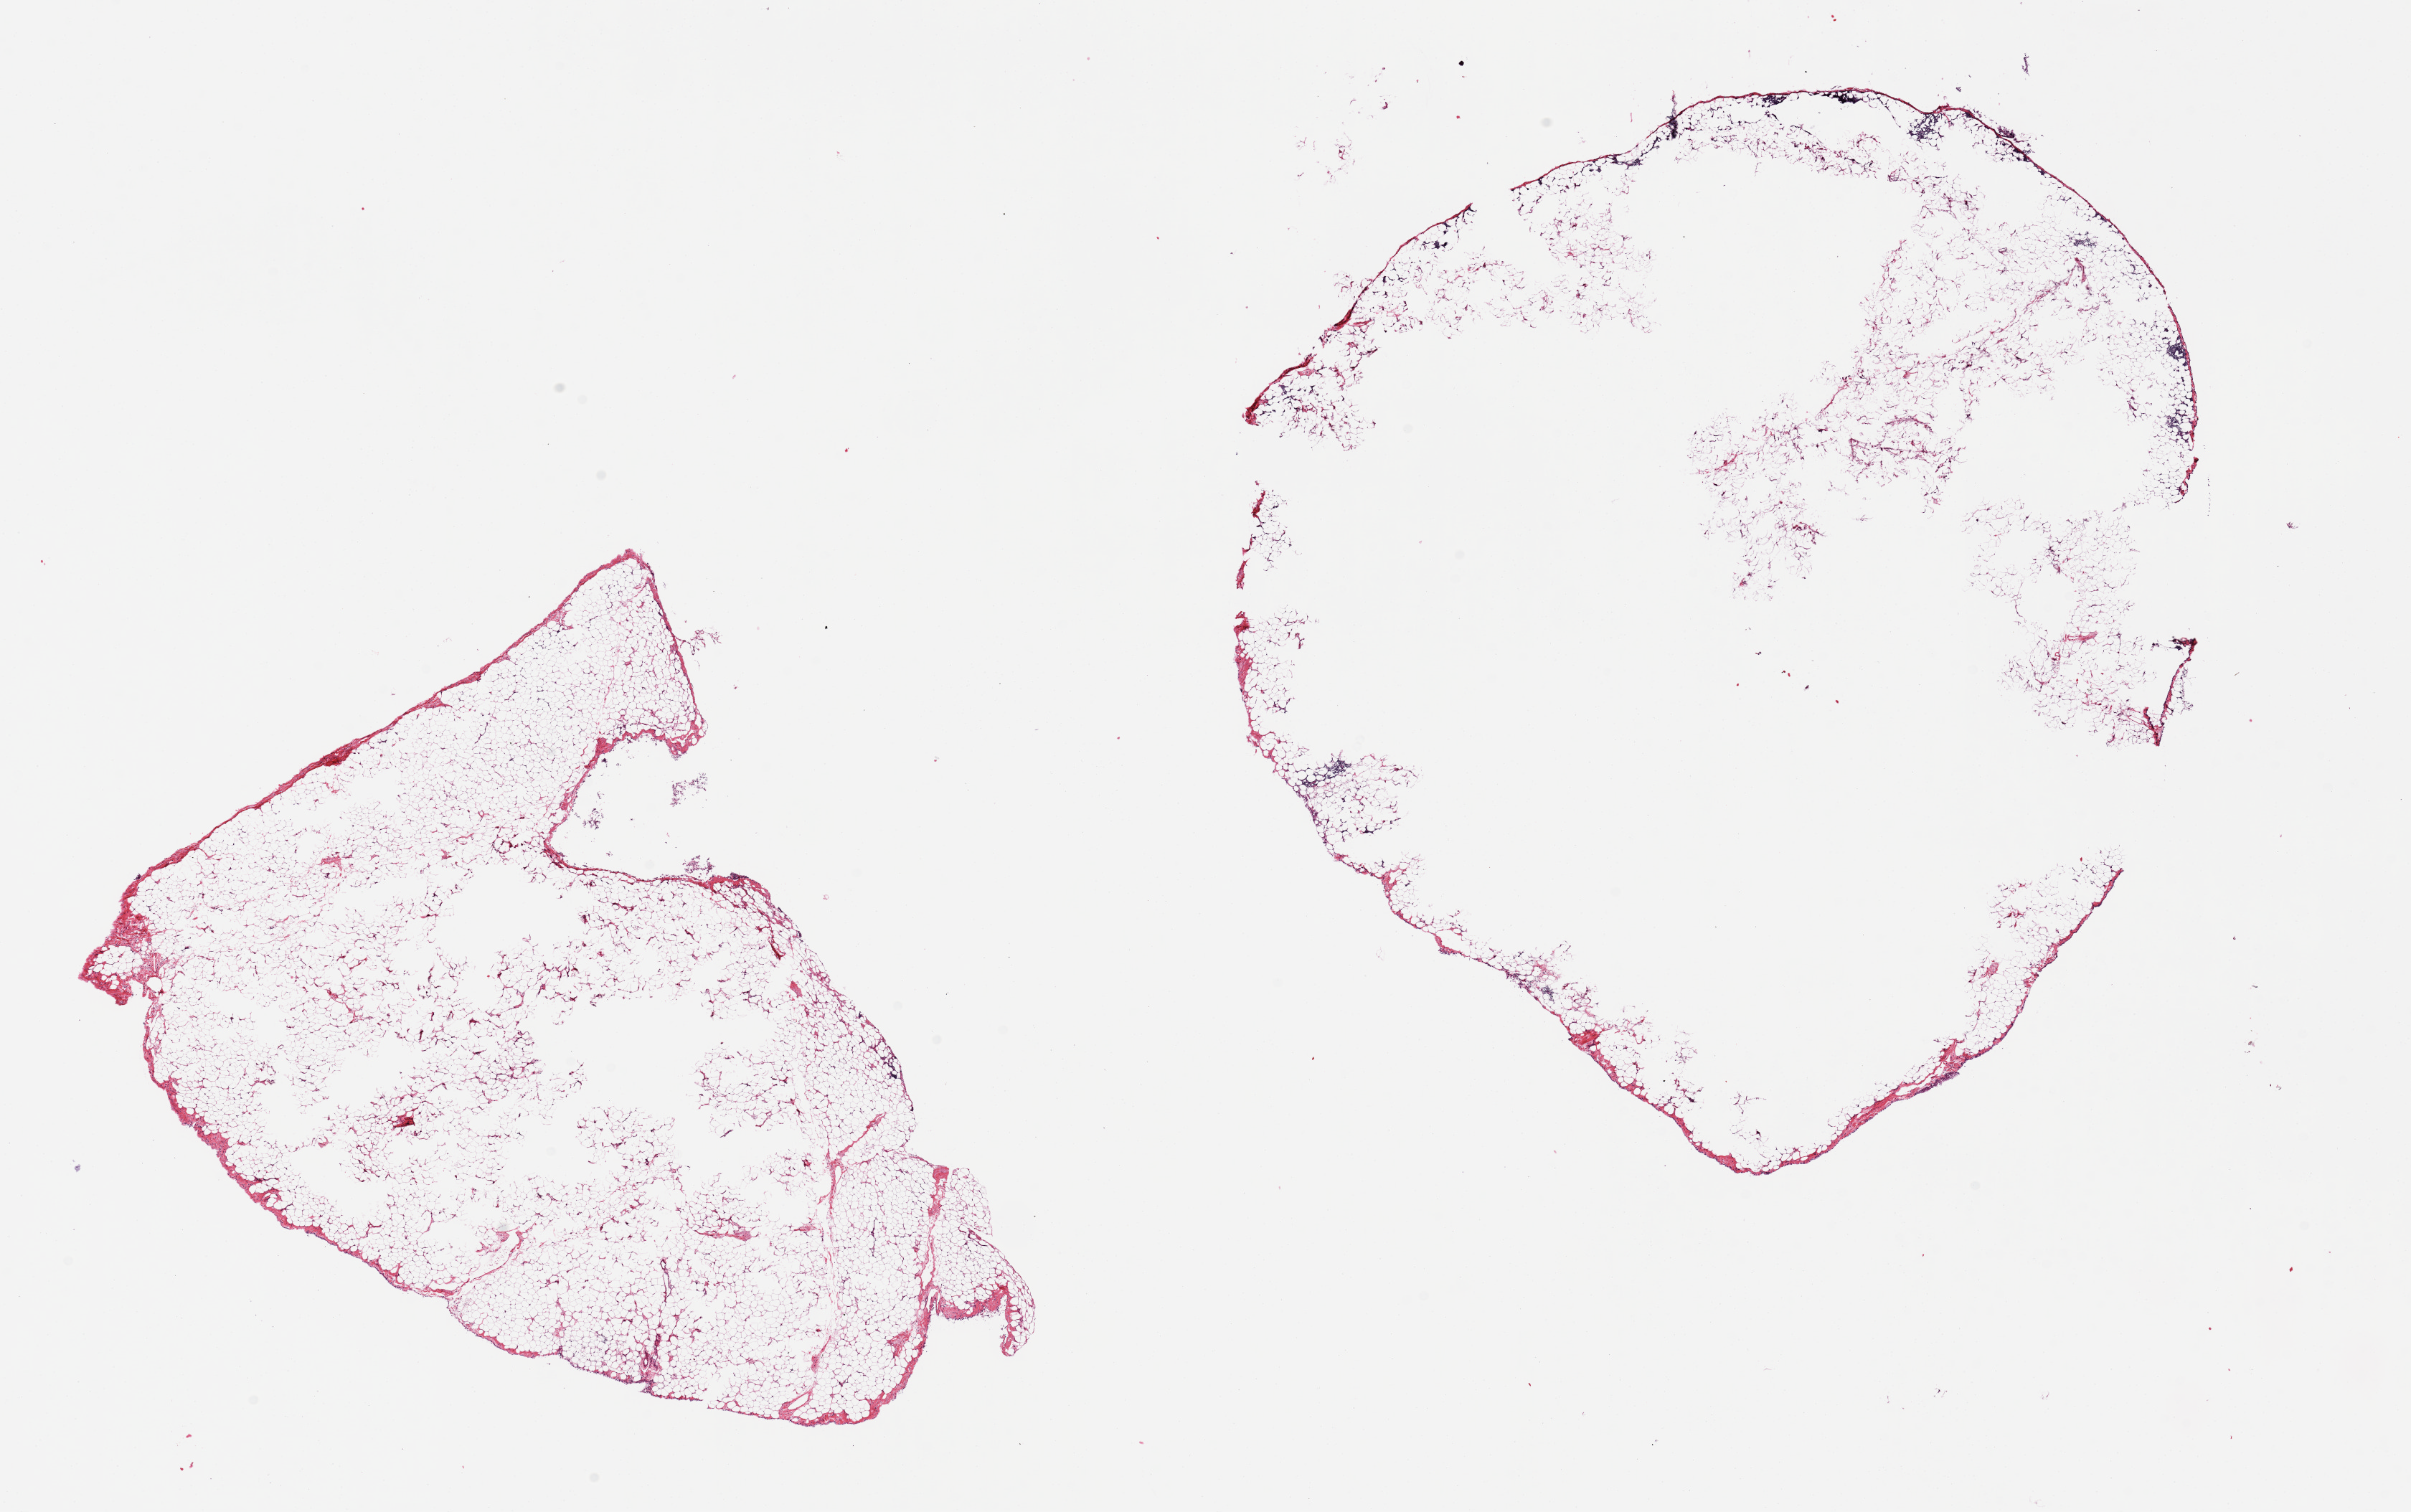
Whole-slide image, H&E stain — whole scanned area (about 26.6 x 16.7 mm) shown as a low-resolution overview. PAXgene-fixed paraffin-embedded (PFPE) section. Sampled site (target tissue): omentum. Tissue donor sample. Male donor.
Reviewer comment on this tissue sample: 2 pieces, fat appears underfixed (not relevant to -26 aliquots).